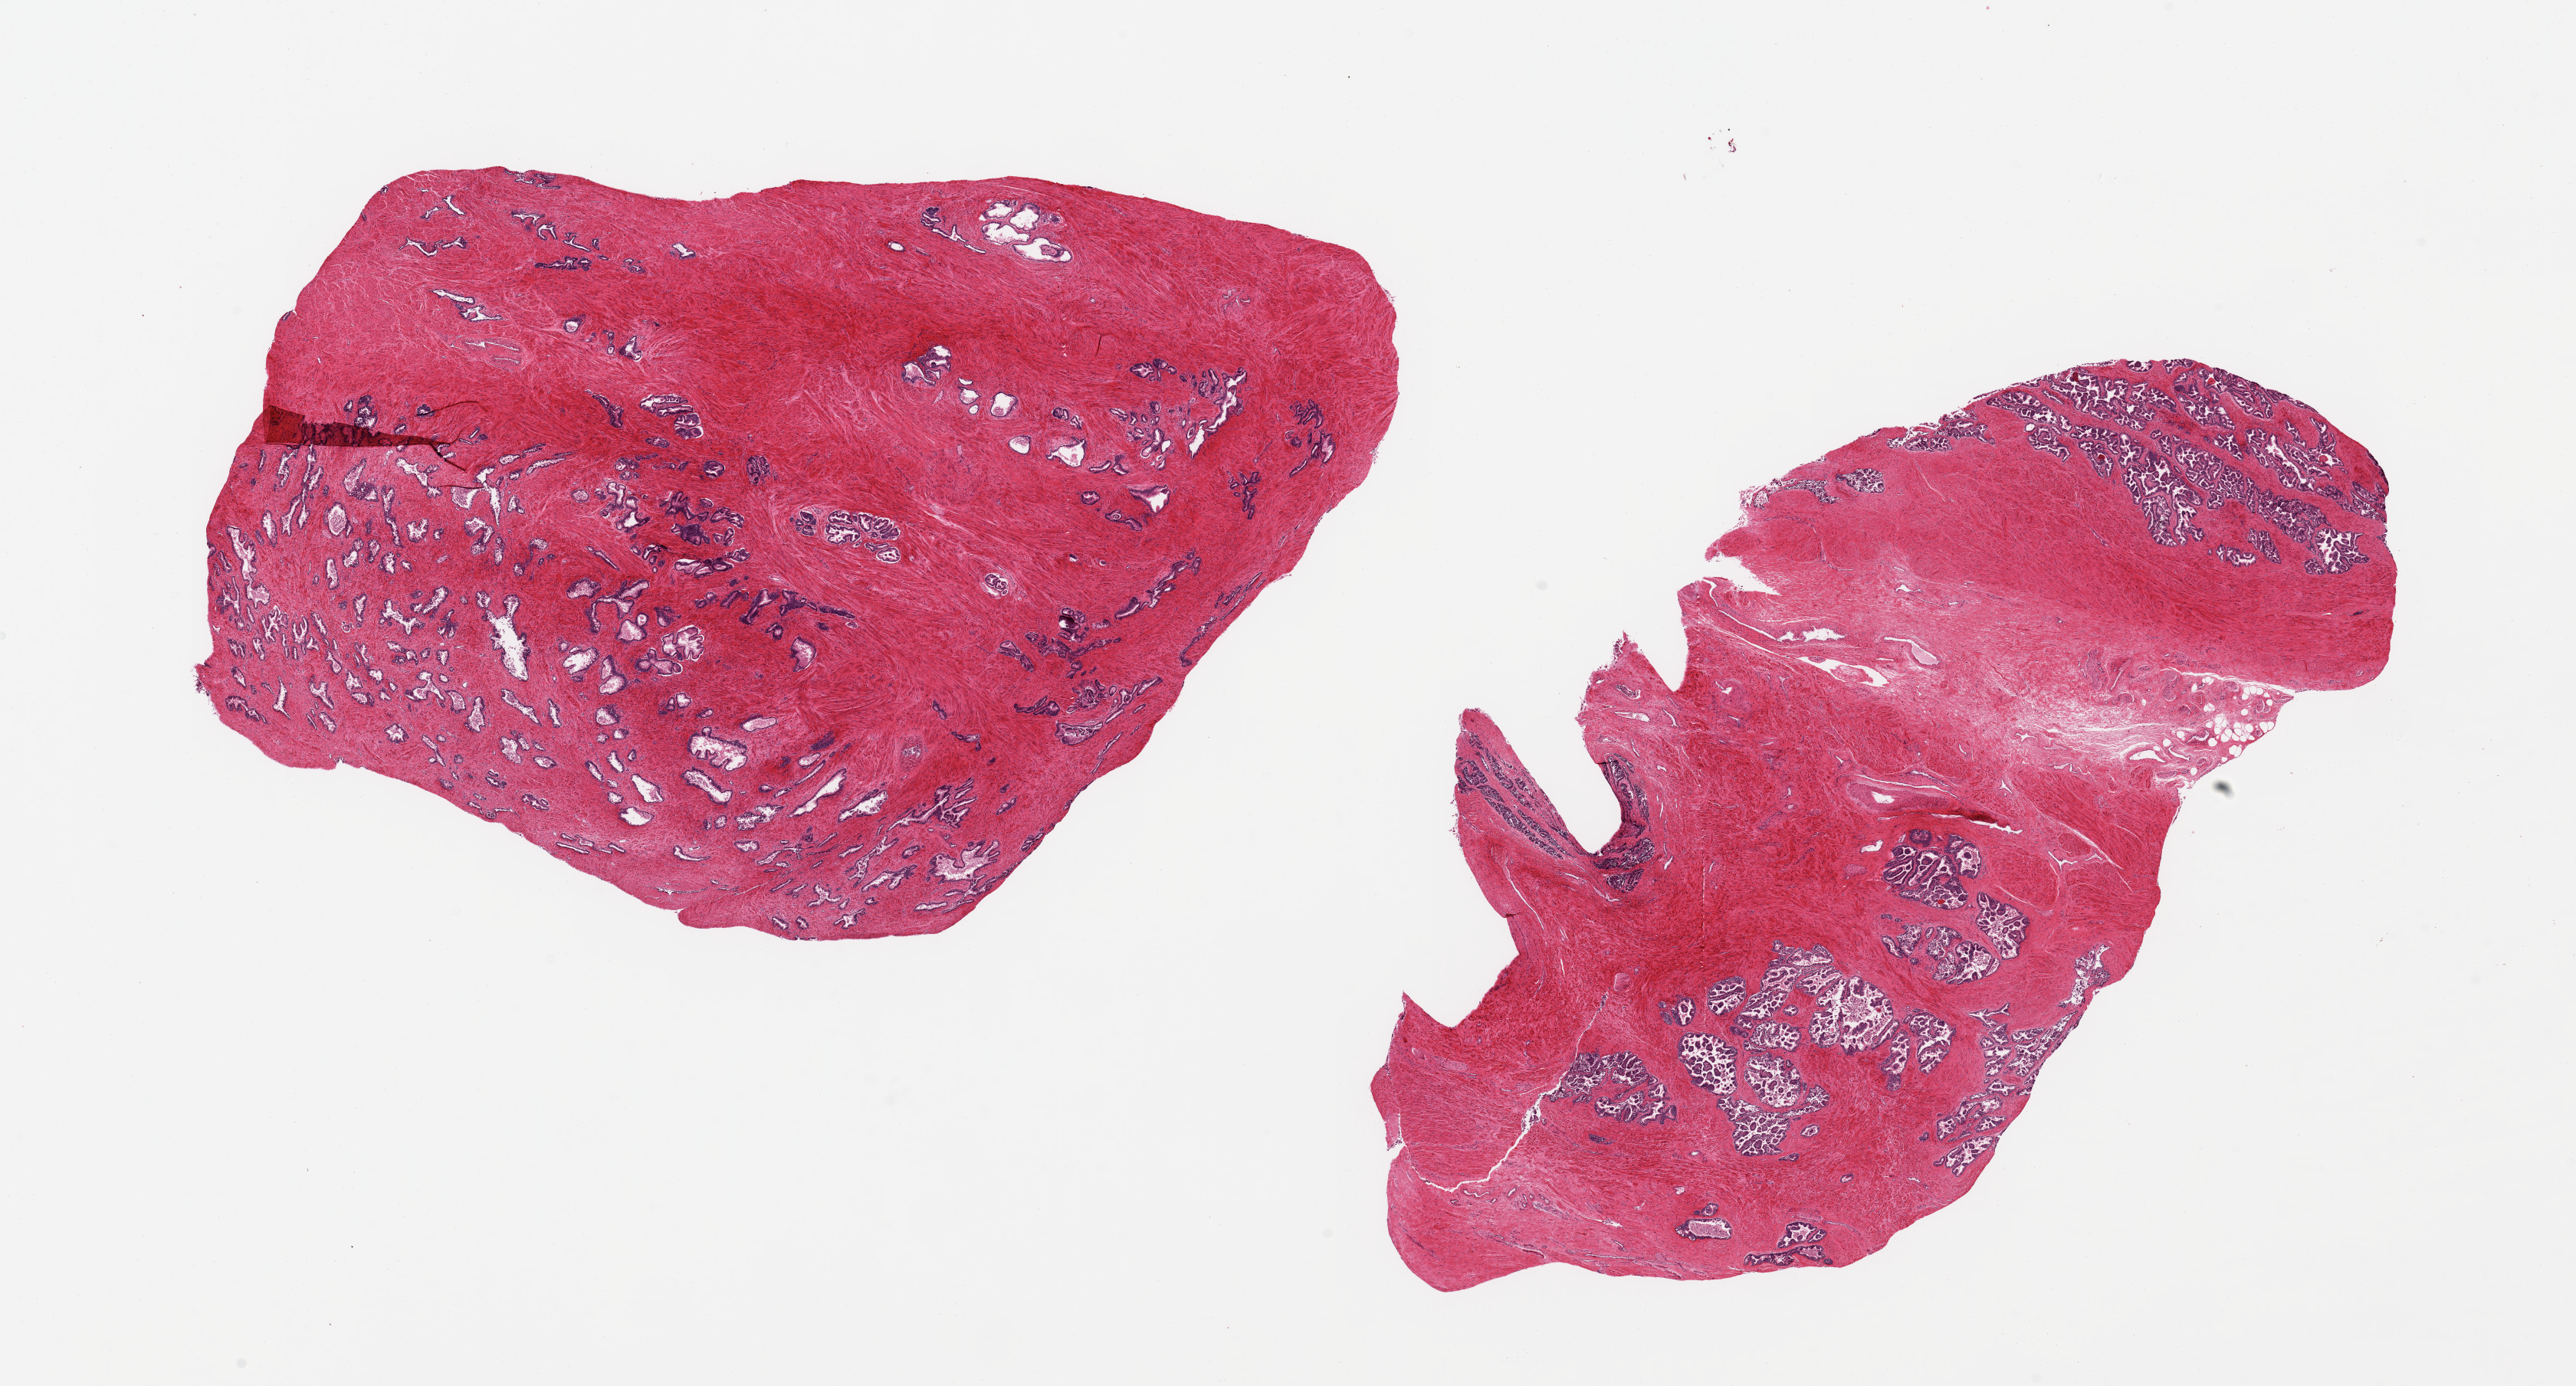
Whole-slide image, haematoxylin and eosin stain, a low-resolution overview of the entire scanned area, about 26.6 x 14.3 mm, PAXgene-fixed, paraffin-embedded tissue, section of prostate (target tissue), donor tissue sample. Donor sex: male.
Pathologist's review note for this sample: 2 pieces; fibromuscular stroma admixed with glands, small portion of seminal vesicle on one piece.